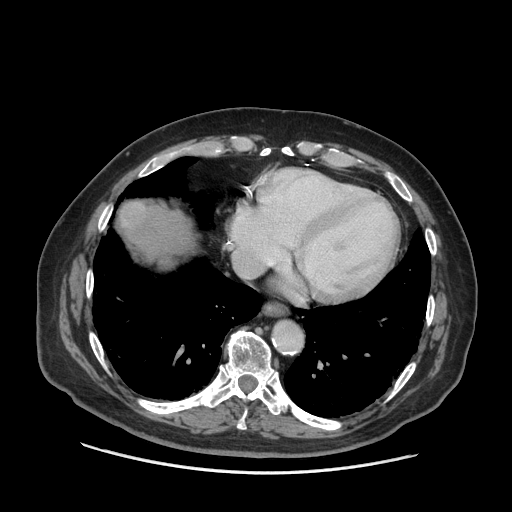
Contrast-enhanced abdominal CT (liver protocol), one axial slice. Slice 66 of 77 in the series (ordered by position). Reconstruction kernel STANDARD. 140 kVp. Soft-tissue window (W 400 / L 40 HU). 2.5 mm slice thickness. 512 × 512 image matrix, field of view 420 × 420 mm. From the clinical record (not read from this slice): diagnosis: hepatocellular carcinoma (patient treated with transarterial chemoembolisation; whether this scan precedes or follows treatment is not stated here); TNM stage (as recorded): Stage-I; Child-Pugh class: A; tumour size: 3.8 cm.
Outlined on this slice (semi-automatic segmentation, software-assisted and operator-edited):
- abdominal aorta: bounding box [x1, y1, x2, y2] px = [273, 323, 302, 352]
- liver parenchyma outside the tumour (the mass and vessels are separate outlines, so this box may not span the whole liver): [118, 200, 192, 266]
- mass: [120, 202, 145, 228]